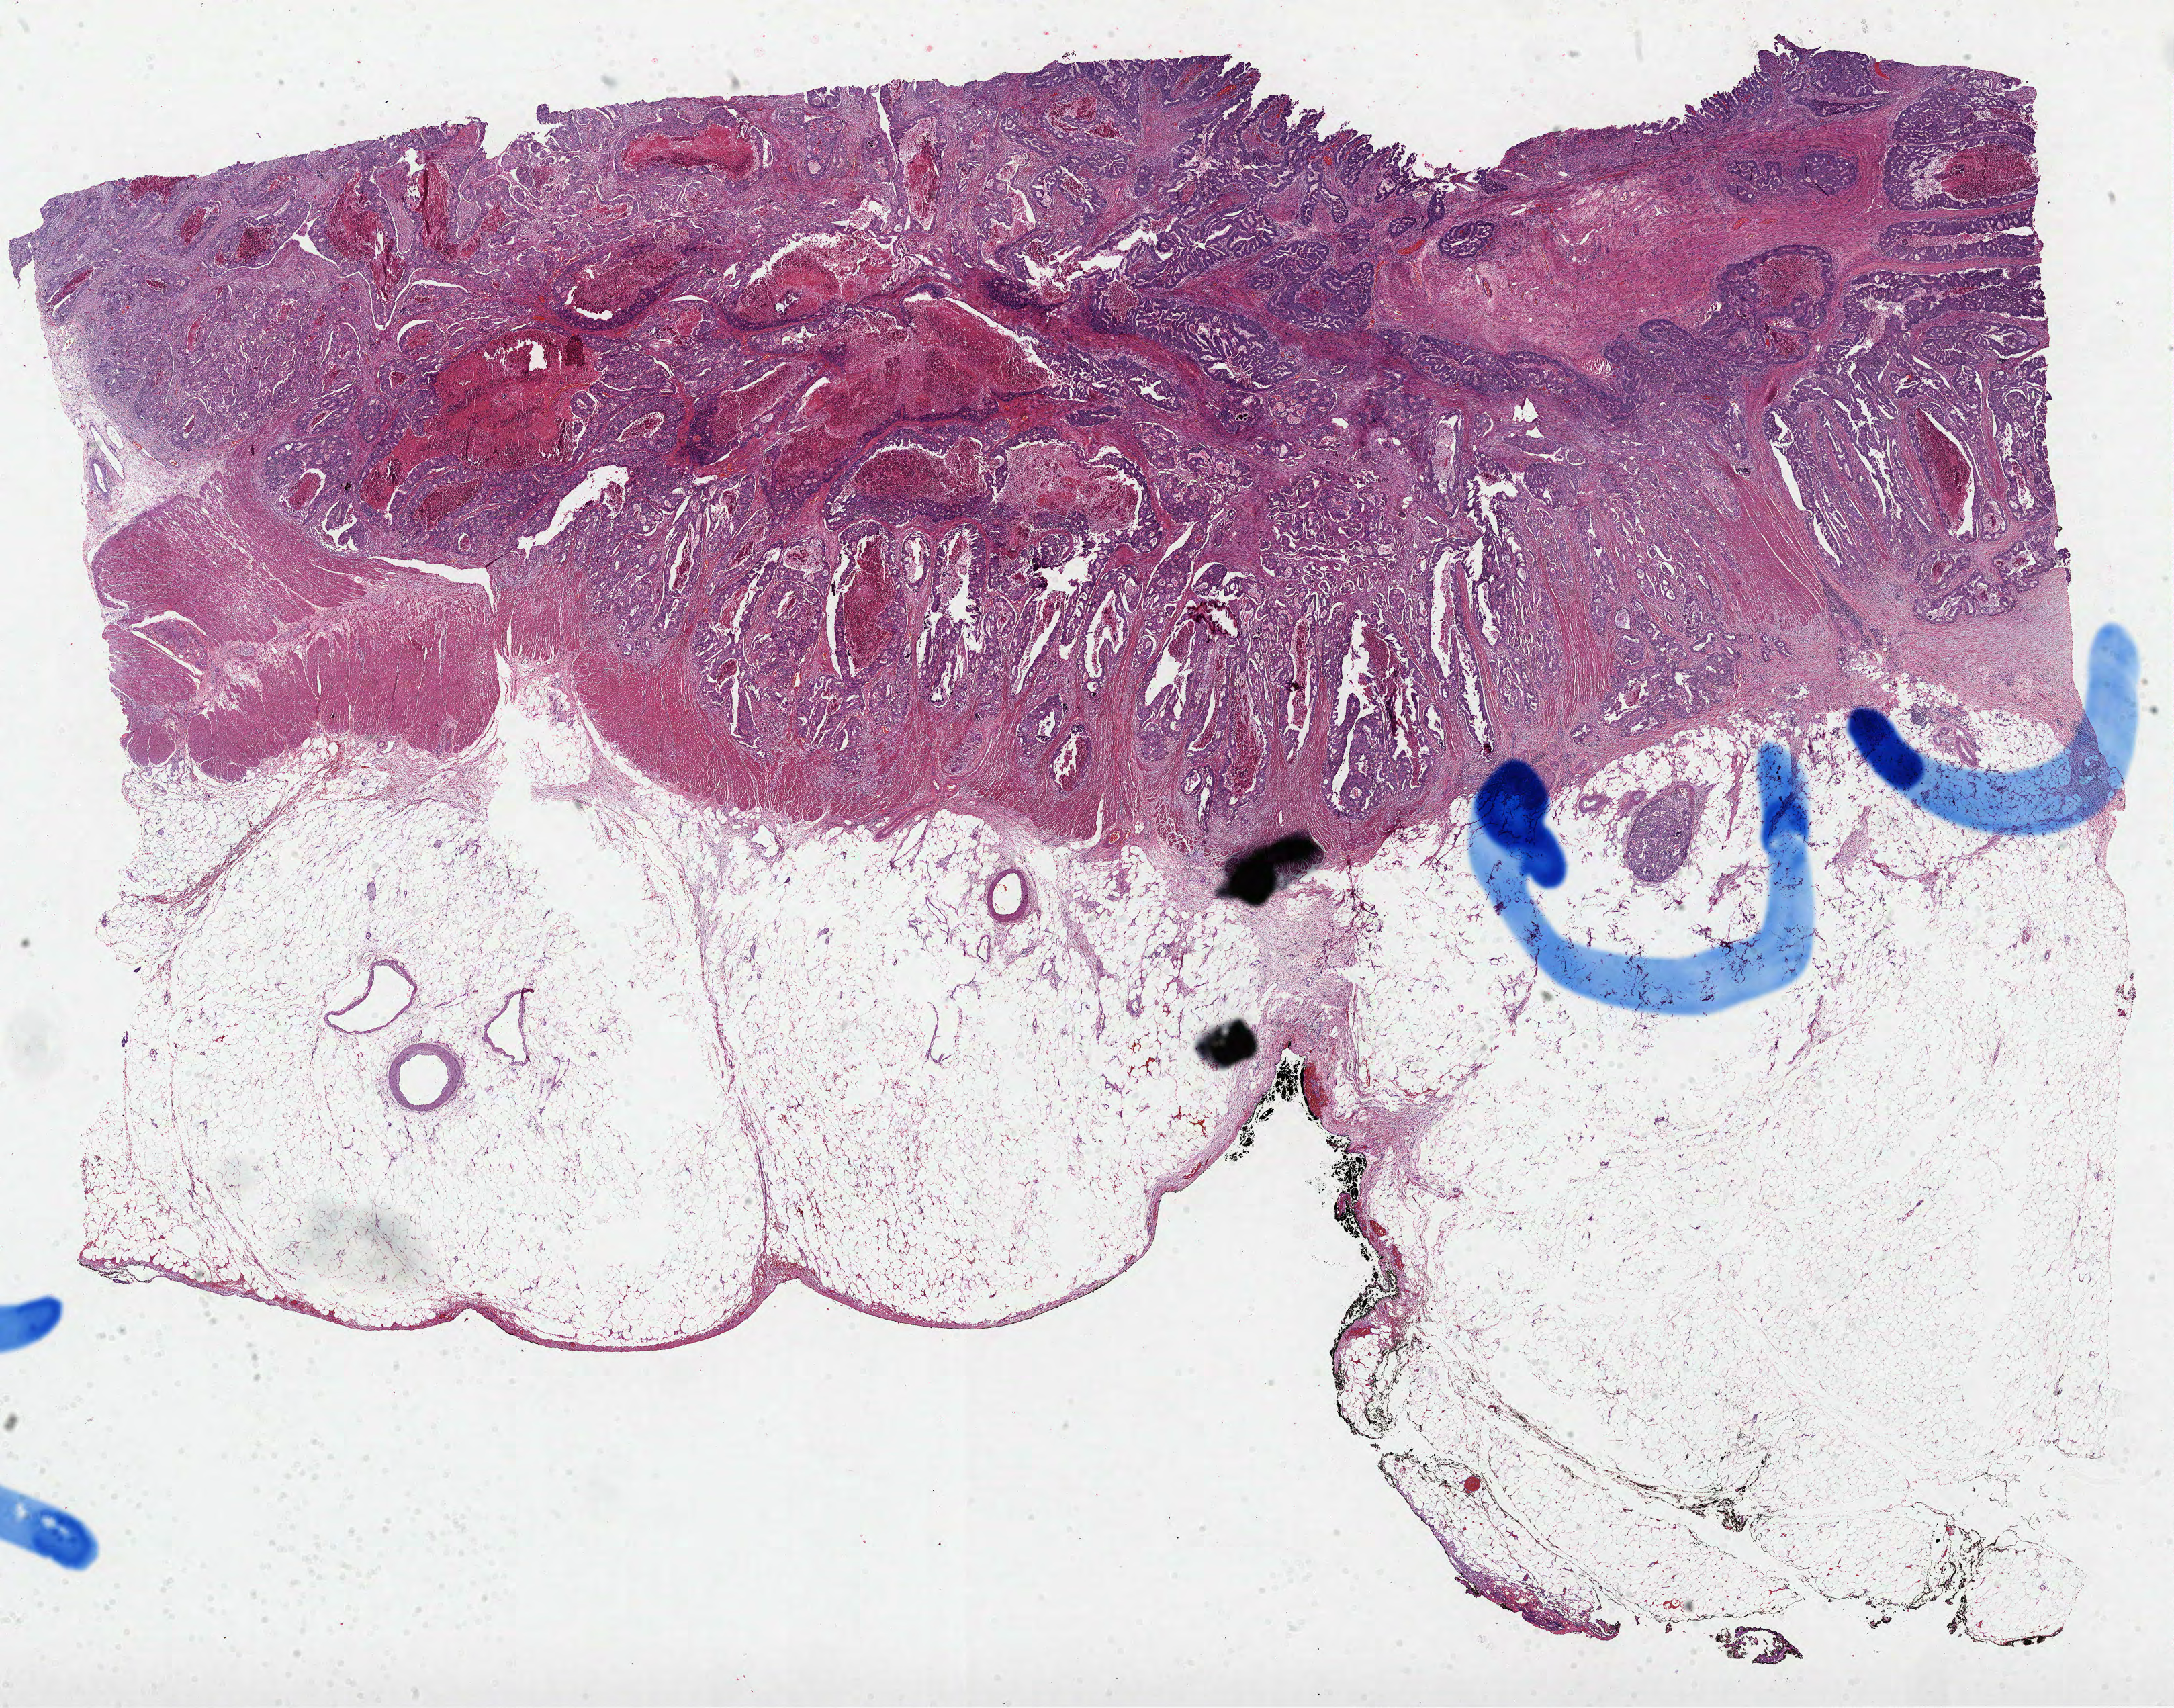
H&E-stained whole-slide image, a low-resolution overview of the entire scanned area, about 26.1 x 20.5 mm; formalin-fixed paraffin-embedded (FFPE) diagnostic section; primary tumour sample from the colon. Male, age 49 years at initial diagnosis.
AJCC pathologic stage: IVA. TNM: T3 N2 M1. Histologic diagnosis: Adenocarcinoma, NOS (rectosigmoid junction). Lymph nodes positive (case pathology): 10 of 12 examined.